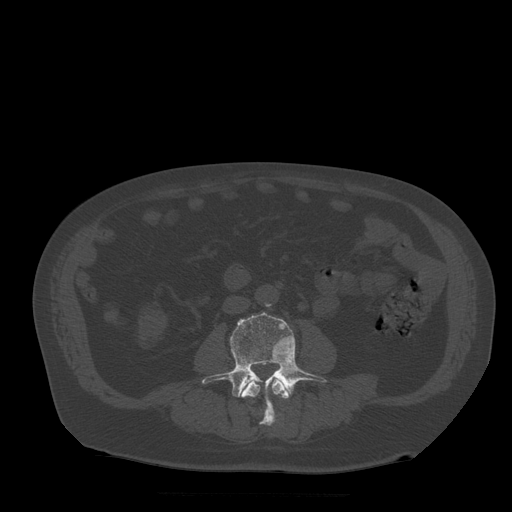
CT including the spine, one axial slice; slice 122 of 522 in the series (ordered by position); bone window (W 1800 / L 400 HU); 512 × 512 image matrix, field of view 420 × 420 mm. Patient age 72 years. From the clinical record (not read from this slice): primary cancer: prostate.
Structures marked on this image (semi-automatic segmentation, software-assisted and operator-edited):
- L3 vertebra: bounding box [x1, y1, x2, y2] px = [241, 379, 289, 427]
- L4 vertebra: [202, 312, 327, 421]